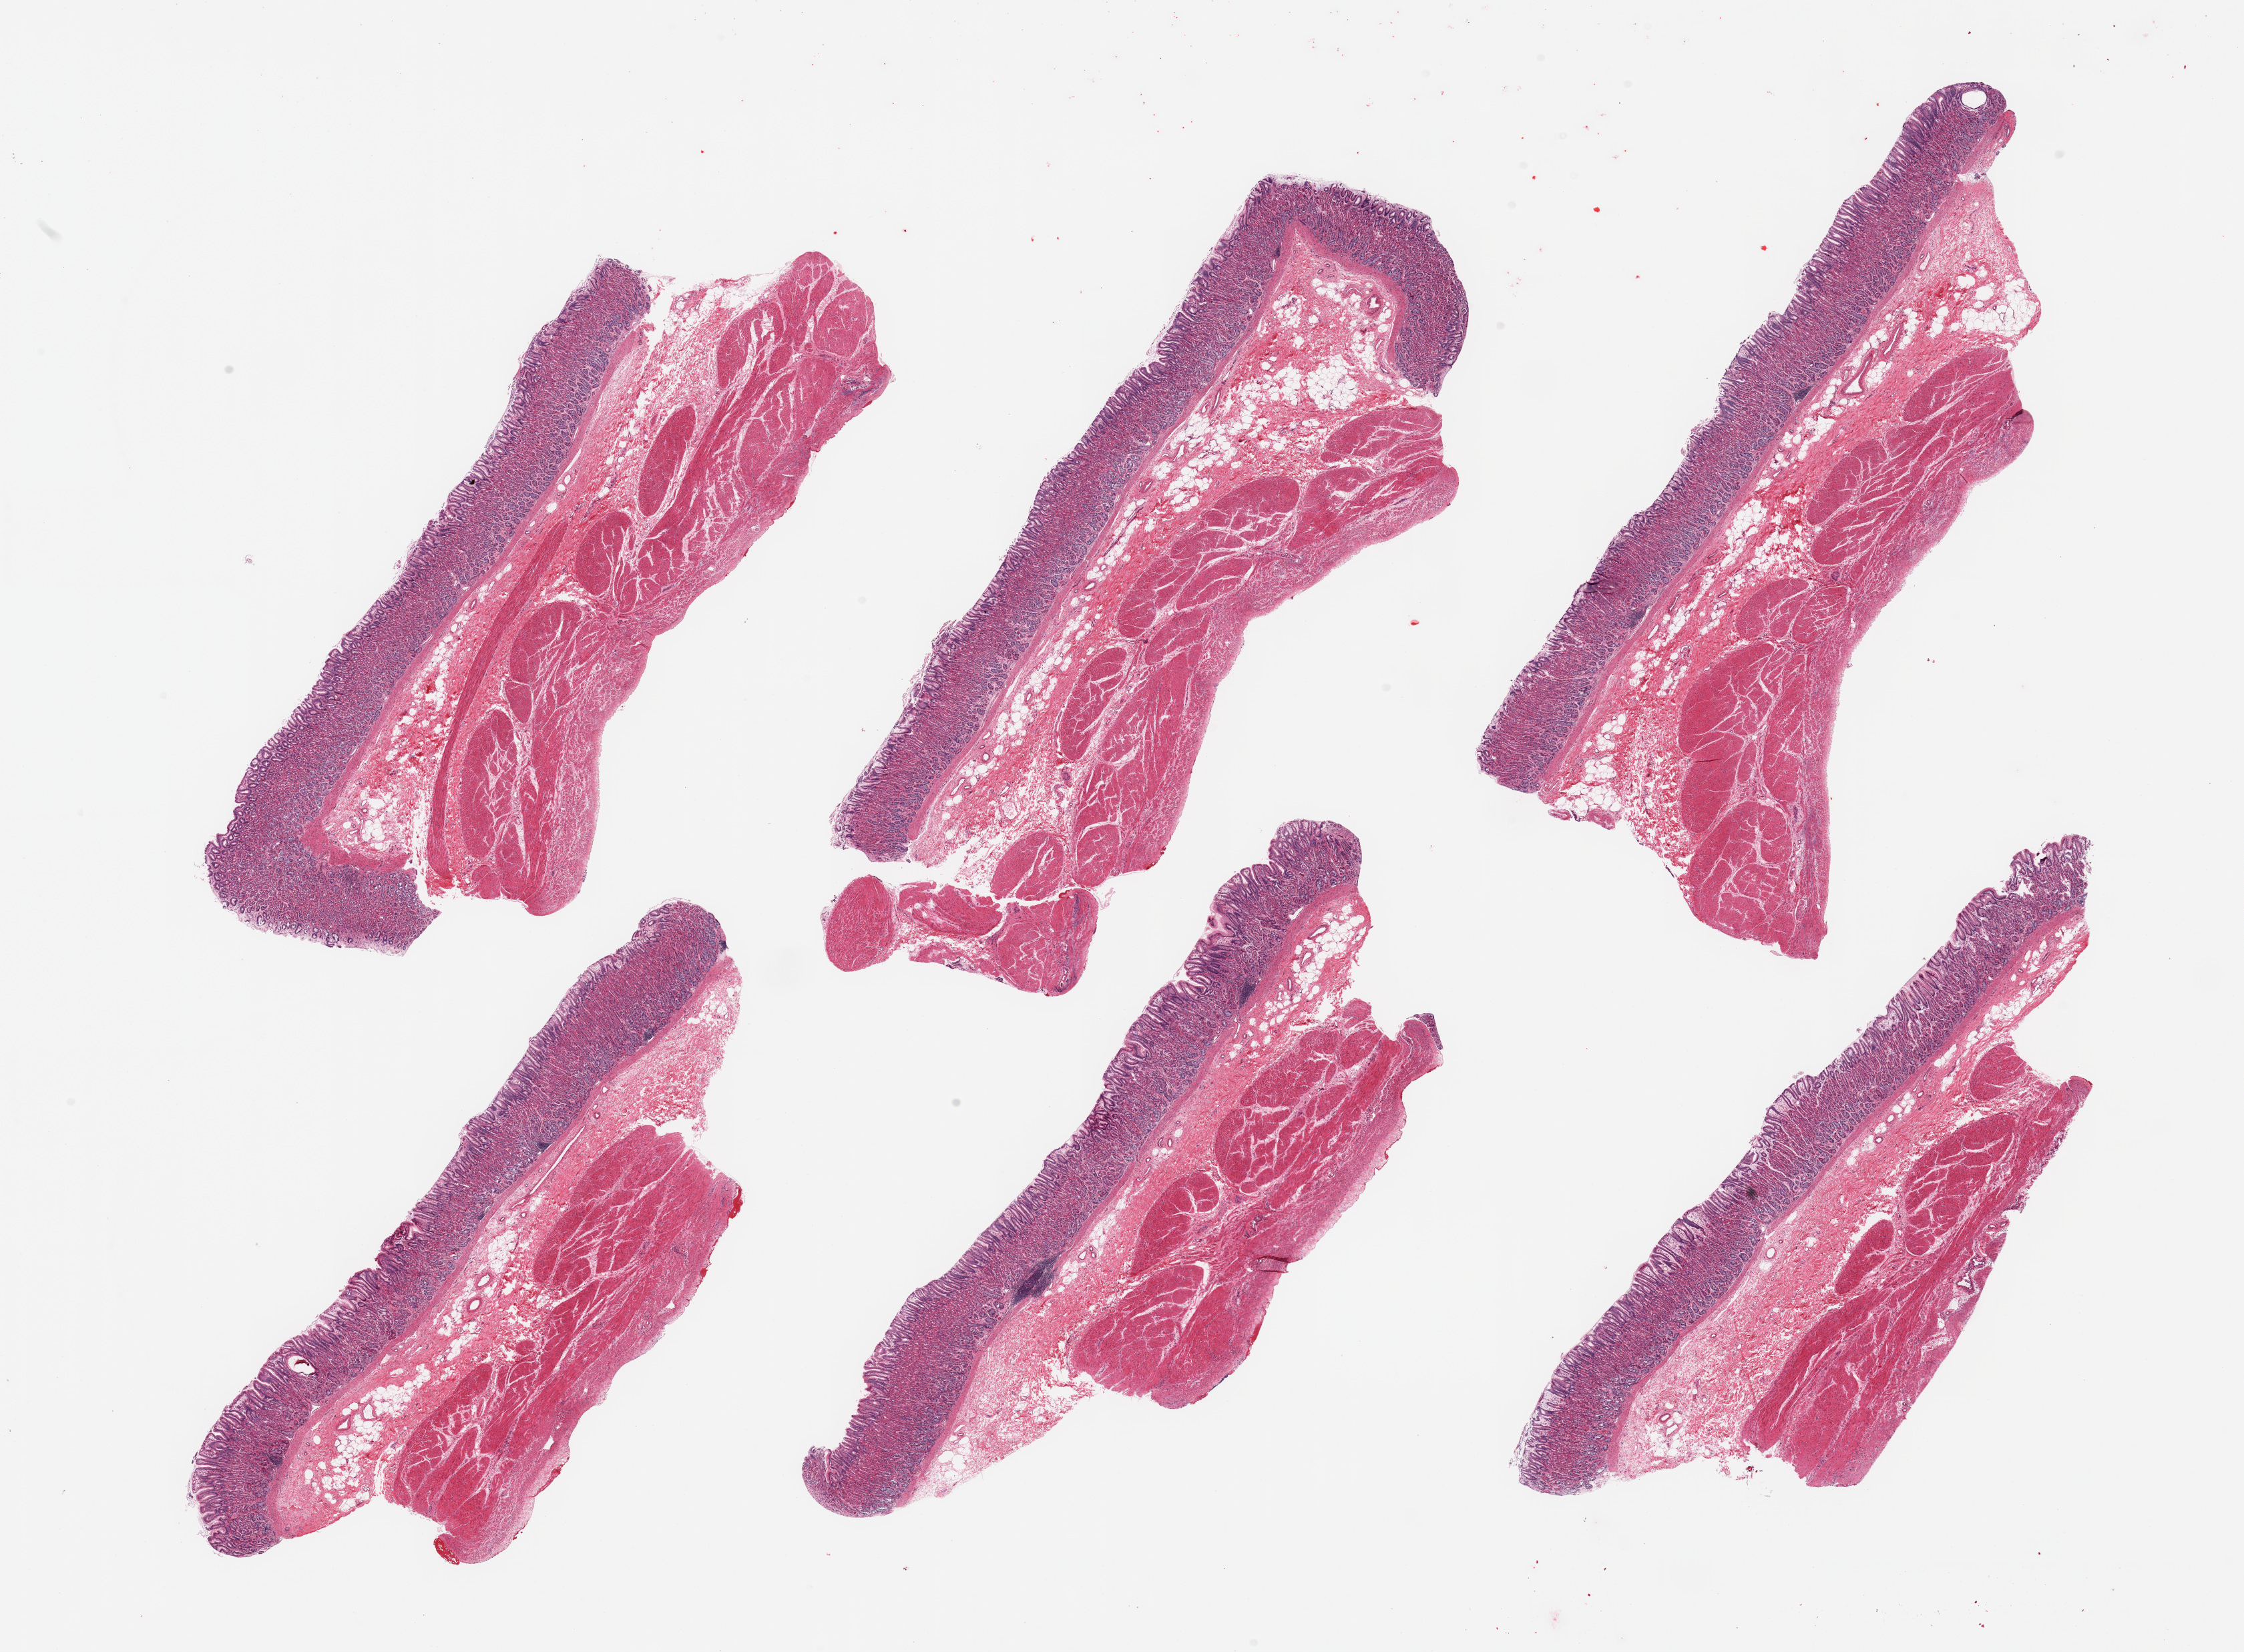
Haematoxylin and eosin whole-slide image, brightfield, a low-resolution overview of the entire scanned area, about 26.6 x 19.6 mm. PAXgene-fixed paraffin-embedded (PFPE) section. Section of stomach (target tissue). Tissue donor sample. Donor sex: male.
* reviewer comment on this tissue sample: 6 pieces; full thickness sections